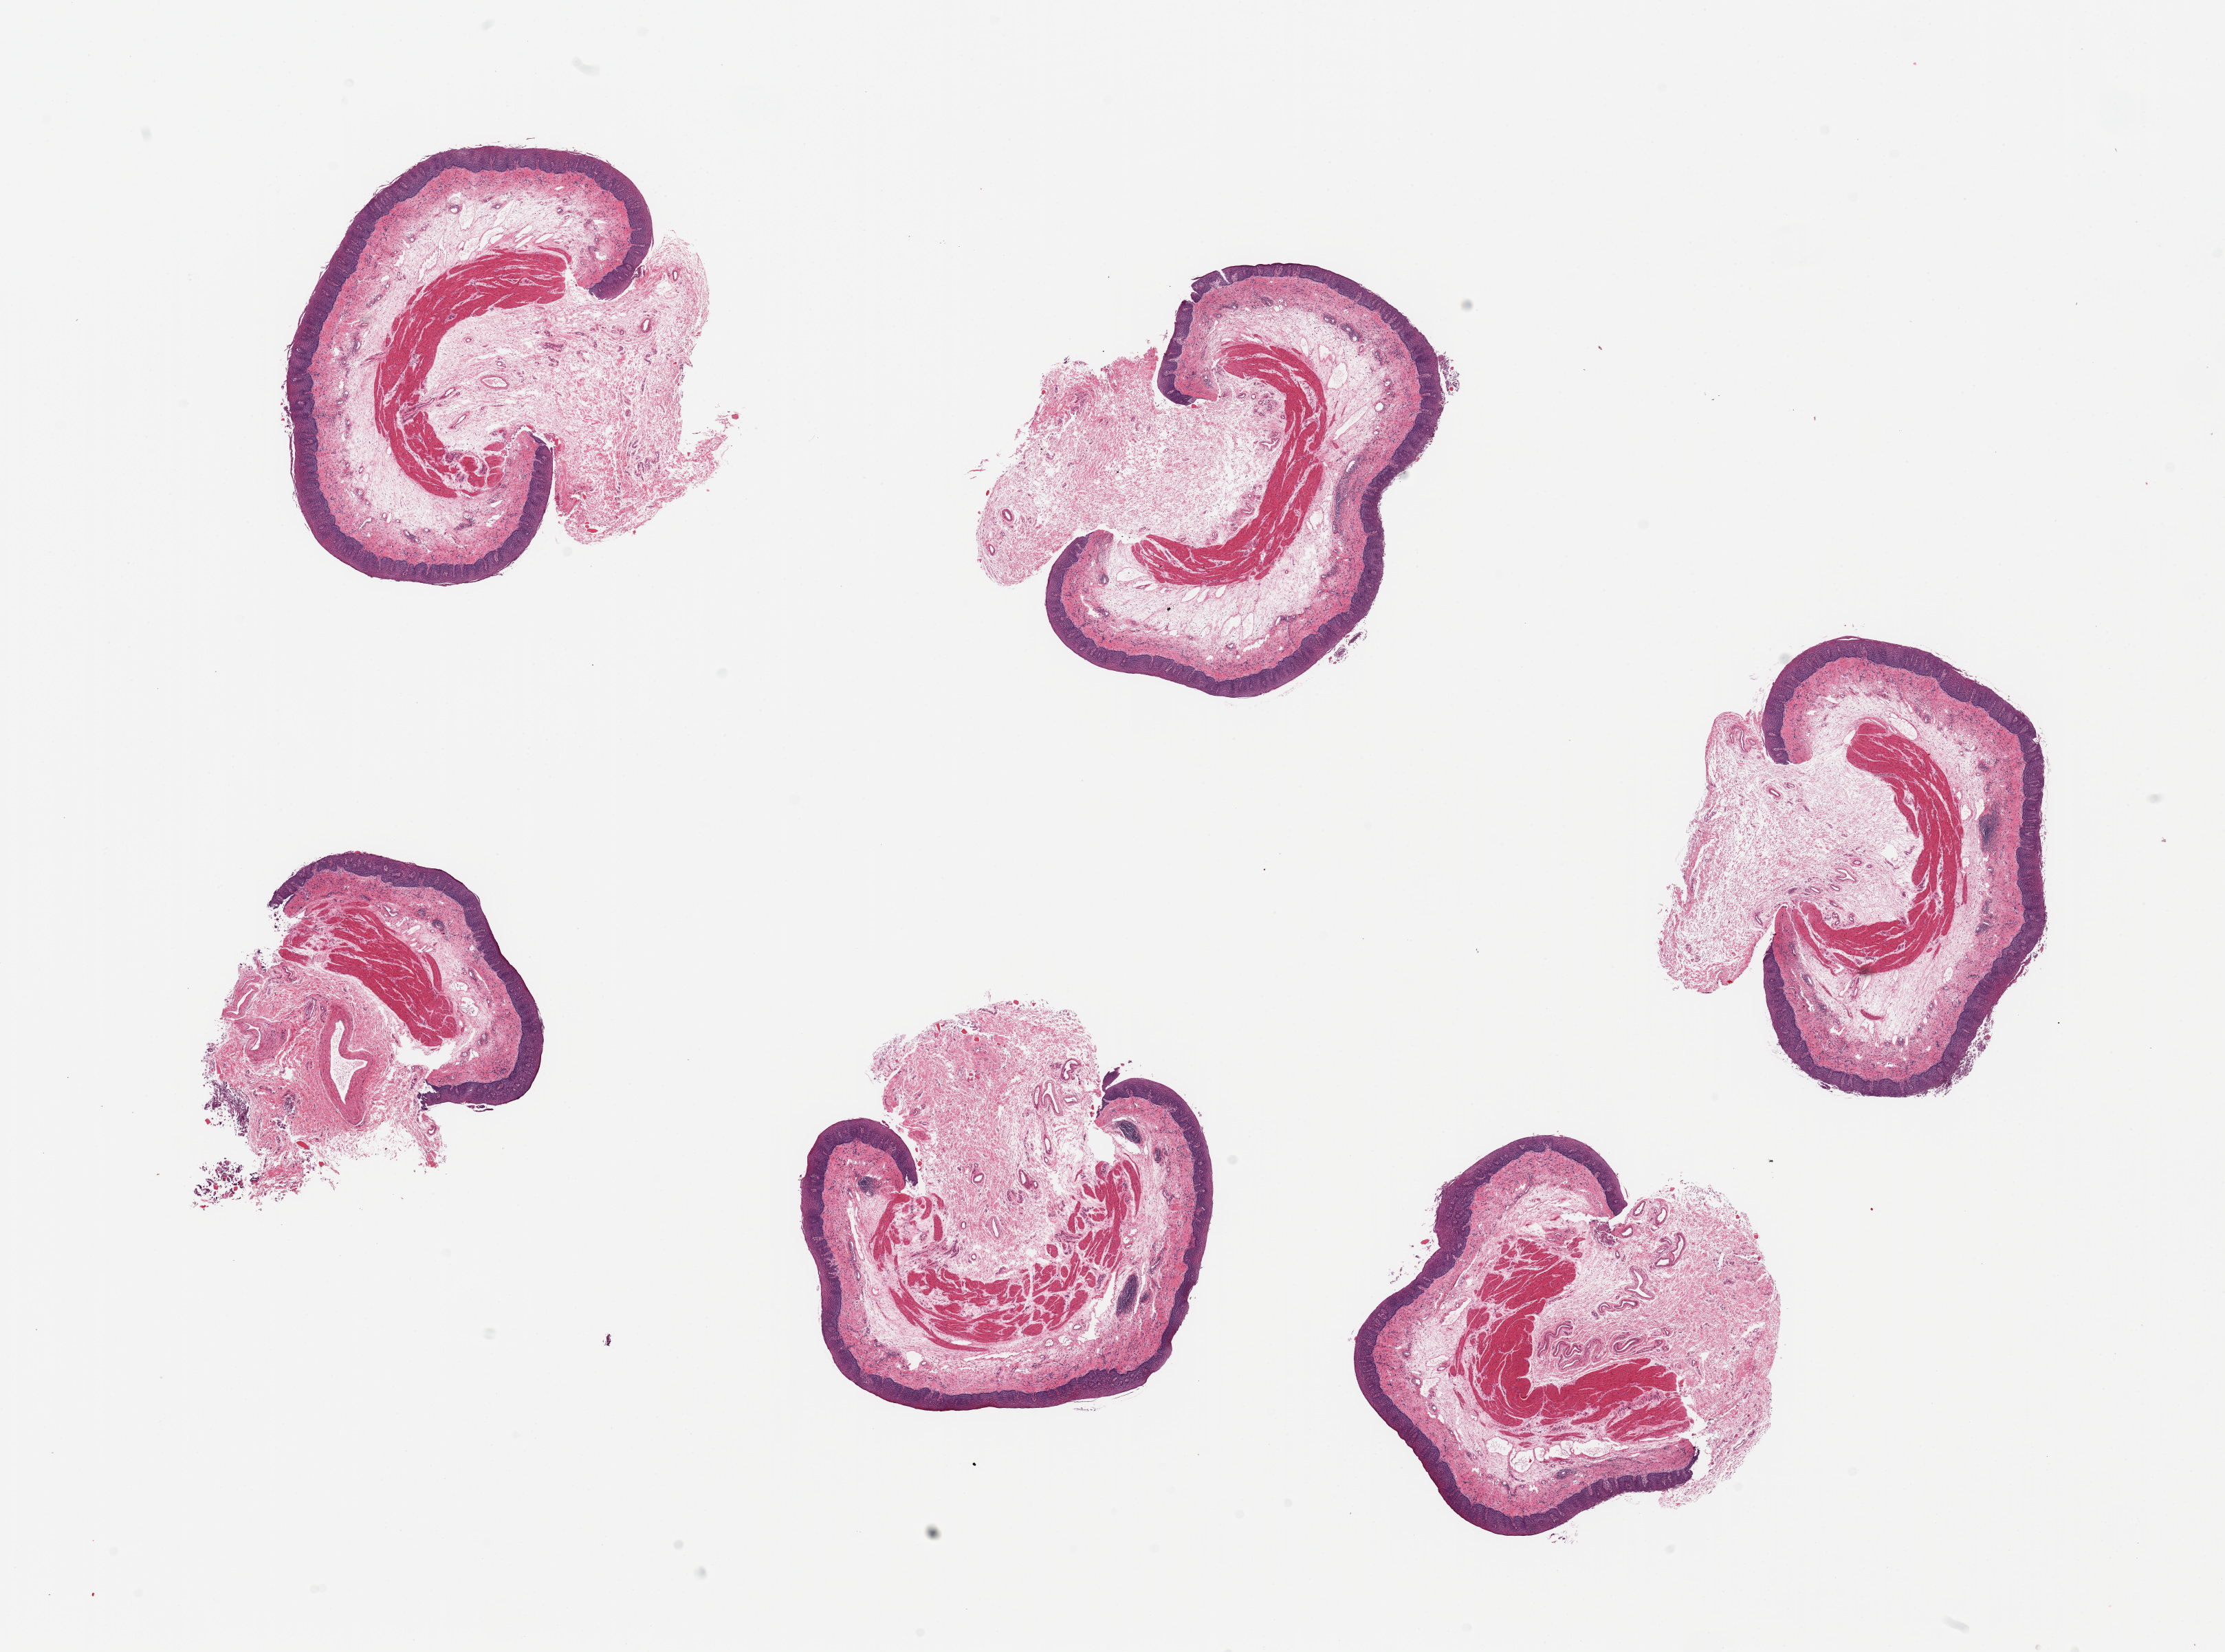
Whole-slide image, hematoxylin and eosin (H&E) stain, brightfield, a low-resolution overview of the entire scanned area, about 25.6 x 19.0 mm; PAXgene-fixed, paraffin-embedded tissue; section of esophageal mucous membrane (target tissue); tissue donor sample.
- pathologist's review note for this sample: 6 pieces; mucosa and abundant submucosa up to 2.7 mm thick; mild chronic esophagitis